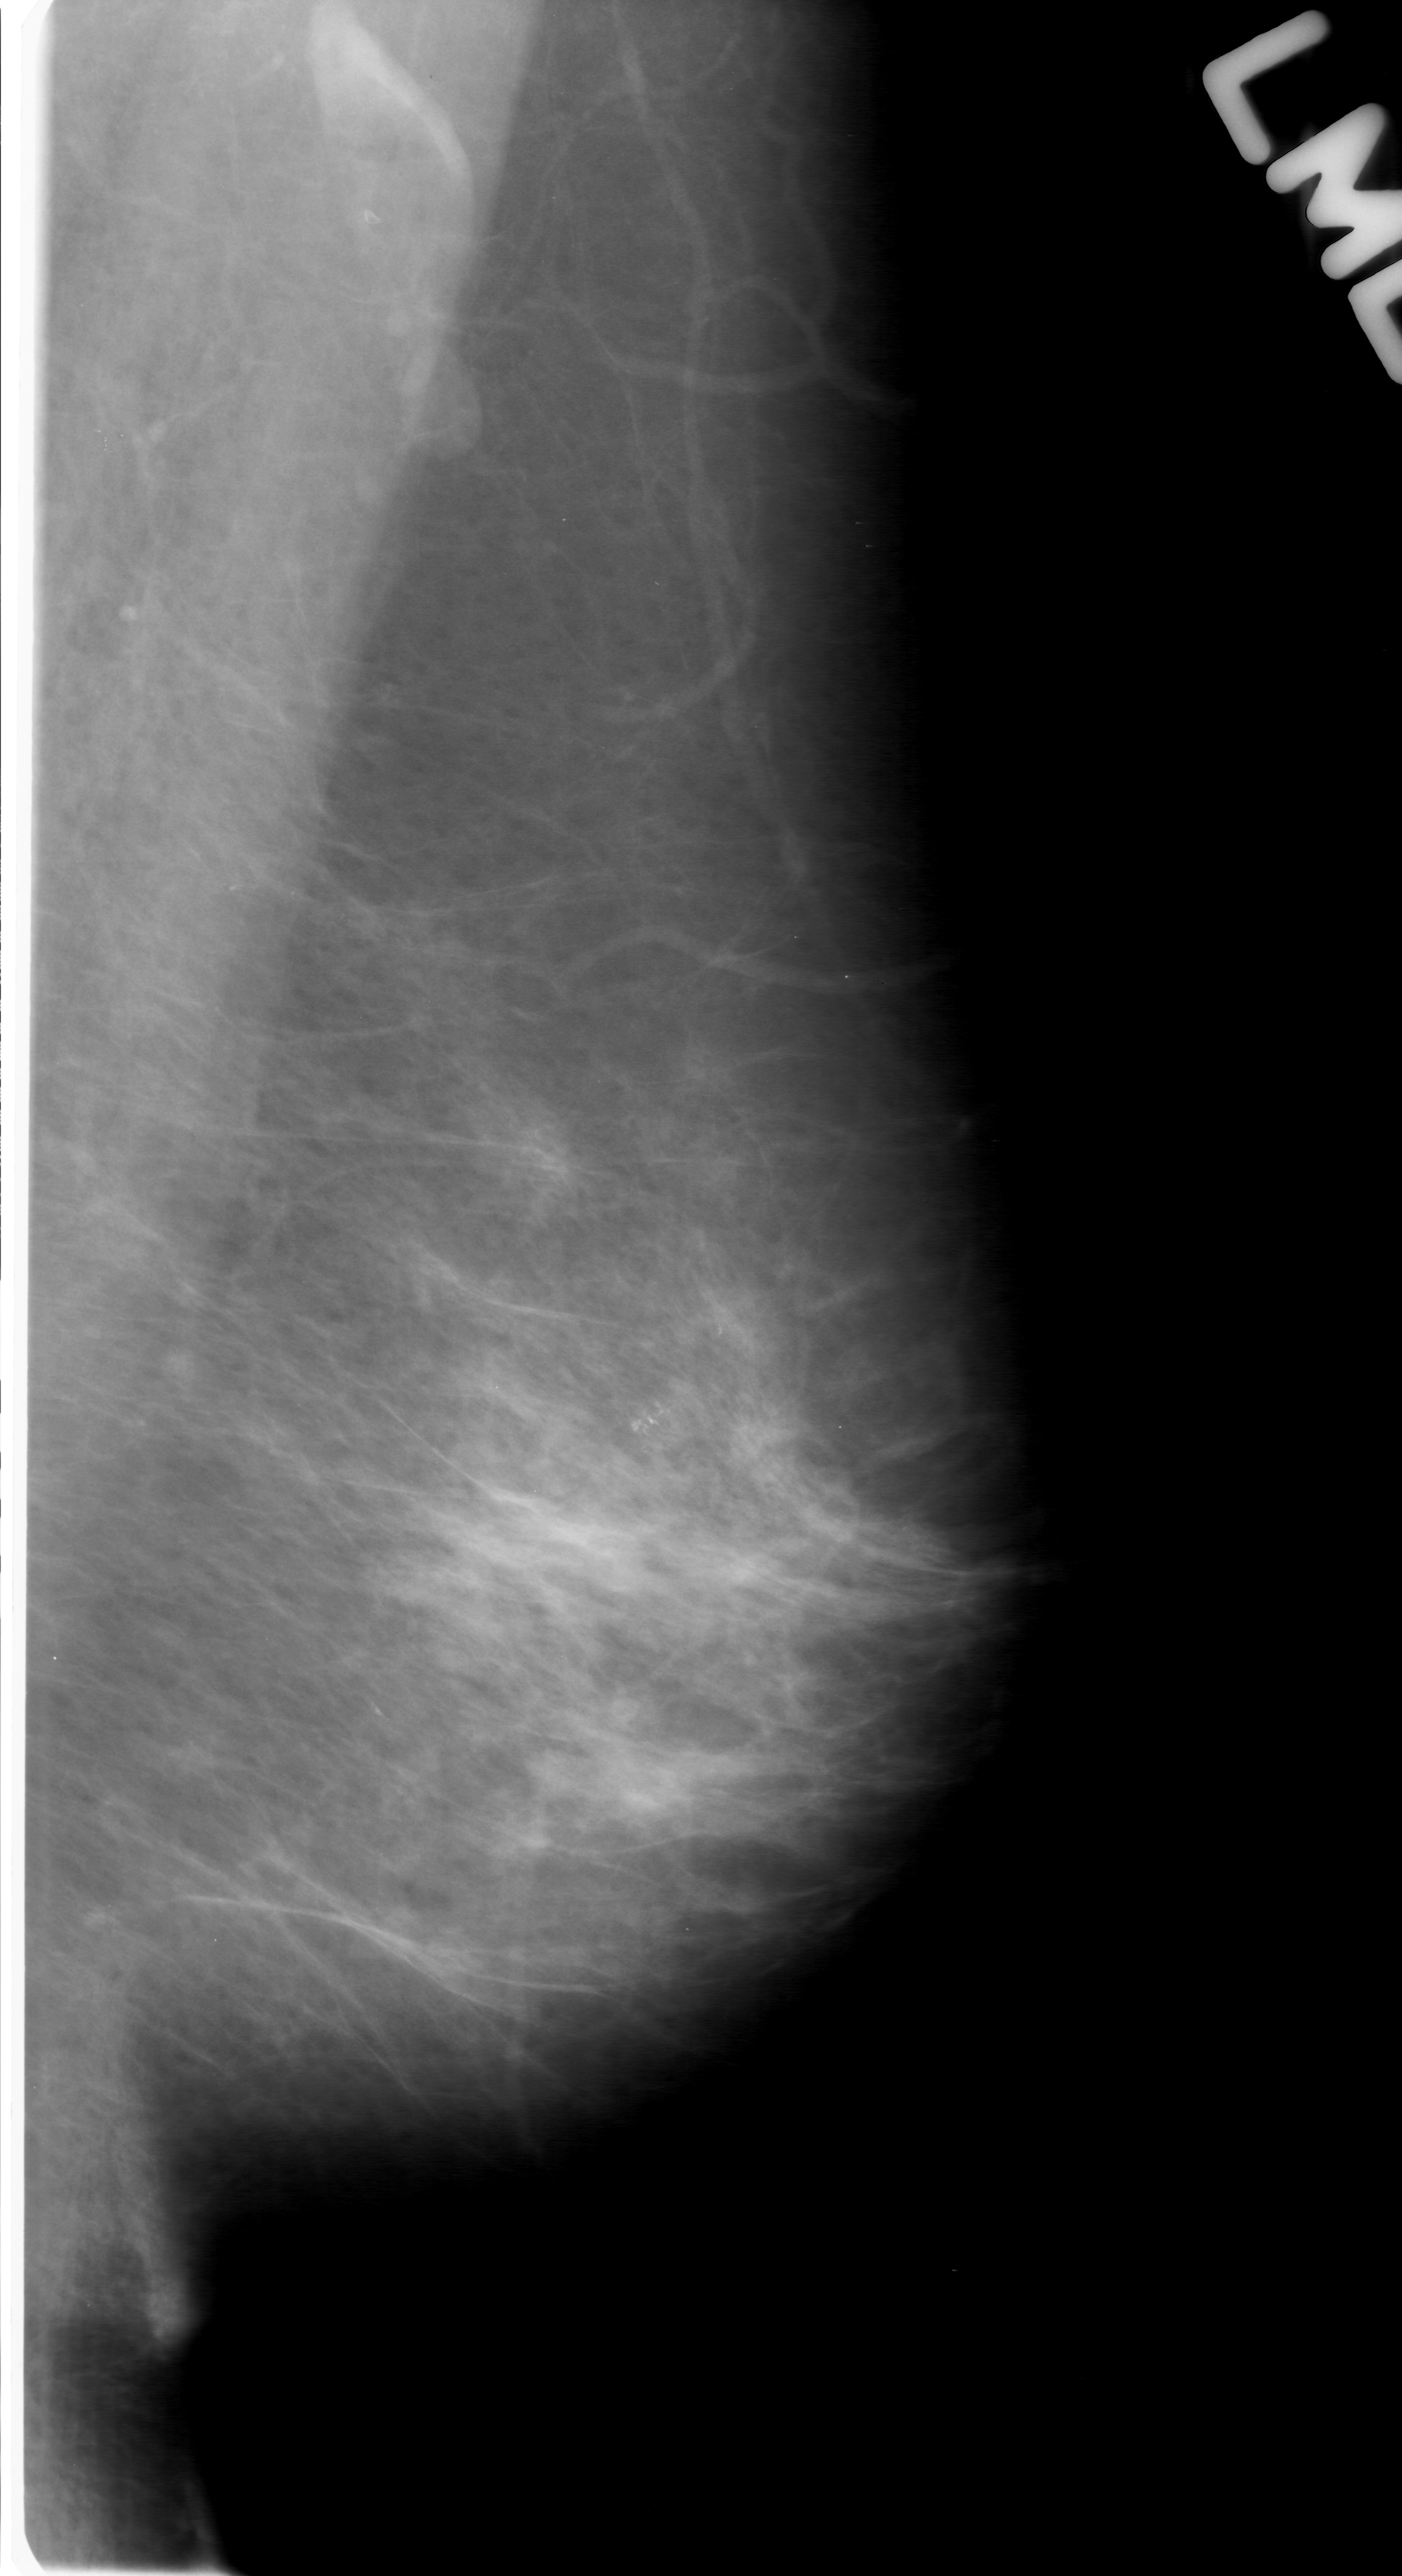
Mammogram (digitized film); left breast; MLO view; breast composition: scattered fibroglandular densities (BI-RADS density category 2 of 4).
Calcifications, morphology pleomorphic, distribution clustered; BI-RADS assessment category 3; pathology result (as recorded, not read from the image): malignant.